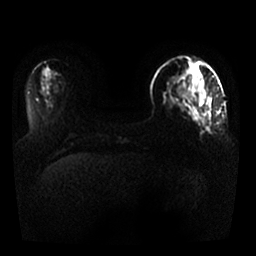
Breast MRI, one axial slice; position 8 of 25 along the scan axis; diffusion-weighted series; image 2 of 4 stored at this slice position (different b-values; order by instance number); 1.5 T; 256 × 256 image matrix. Female patient.
Annotated regions visible in this slice (outlined manually by an expert reader):
- tumour on diffusion-weighted imaging: bounding box [x1, y1, x2, y2] px = [200, 98, 205, 106]